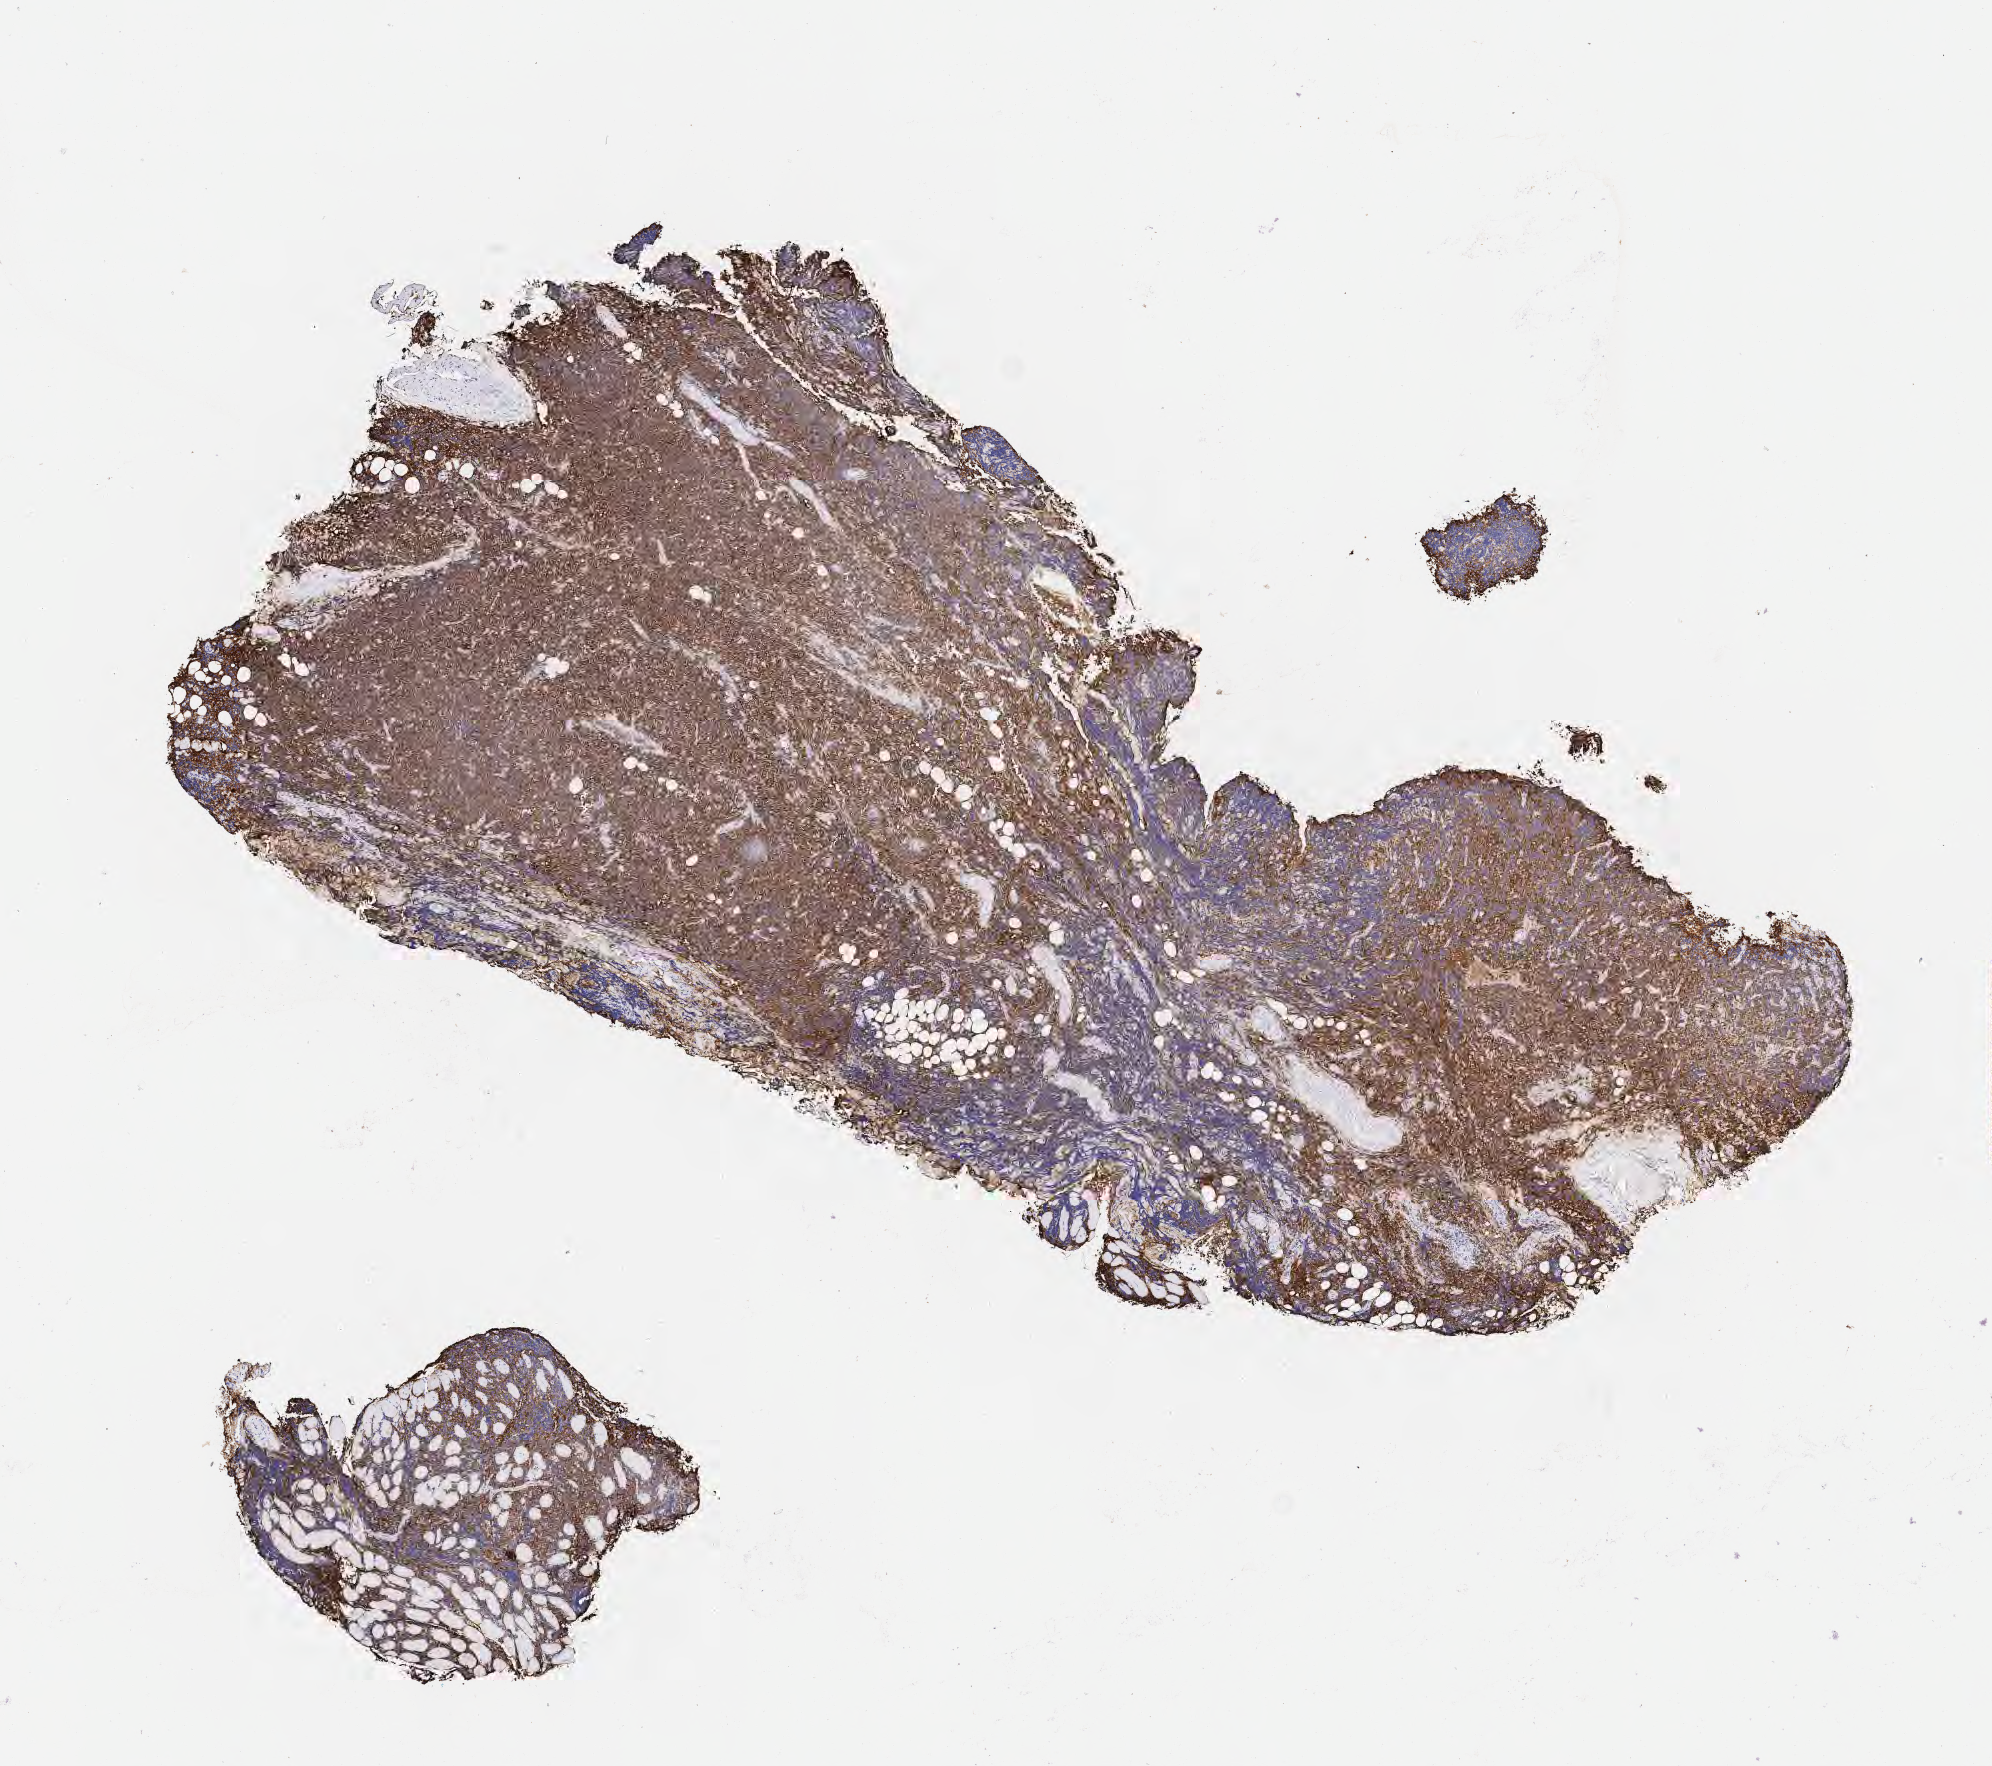
Immunohistochemistry (IHC) whole-slide image stained for CD20, whole scanned area (about 8.0 x 7.1 mm) shown as a low-resolution overview, specimen: tumor tissue. Male patient, 67 years old.
Diagnosis: Diffuse large B-cell lymphoma, NOS.